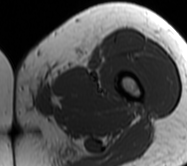
MRI of an extremity soft-tissue mass, one axial slice. Slice 9 of 62 in the series (ordered by position). MR volume resampled by the dataset authors to the PET/CT grid (not the native acquisition matrix). 3.27 mm slice thickness. 187 × 166 image matrix, field of view 183 × 162 mm. Female patient. Case-level facts recorded for this patient, not image findings: histological type: leiomyosarcoma; grade: high; site of the primary tumour: groin.
Outlined on this slice (expert contour drawn on MRI and transferred to this co-registered scan by the dataset authors):
- gross tumour volume including surrounding oedema: box from (x=13, y=71) to (x=58, y=116) px